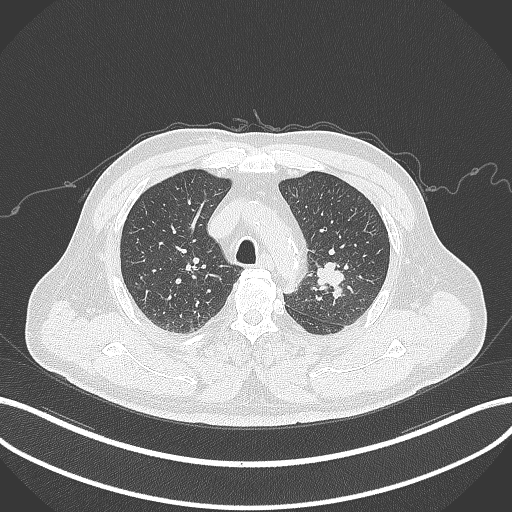
Chest CT, one axial slice. Position 232 of 286 along the scan axis. Reconstruction kernel B70f. 120 kVp. Lung window (W 1500 / L -600 HU). 1 mm slice thickness. 512 × 512 image matrix, field of view 400 × 400 mm. Male patient, age 67 years. Case-level facts recorded for this patient, not image findings: clinical TNM (as recorded): T2a N1 M0.
Annotated regions visible in this slice (rectangle marked by the reading radiologist):
- lung tumour (recorded histology: adenocarcinoma): bounding box <315,257,347,293> (left, top, right, bottom; pixels)